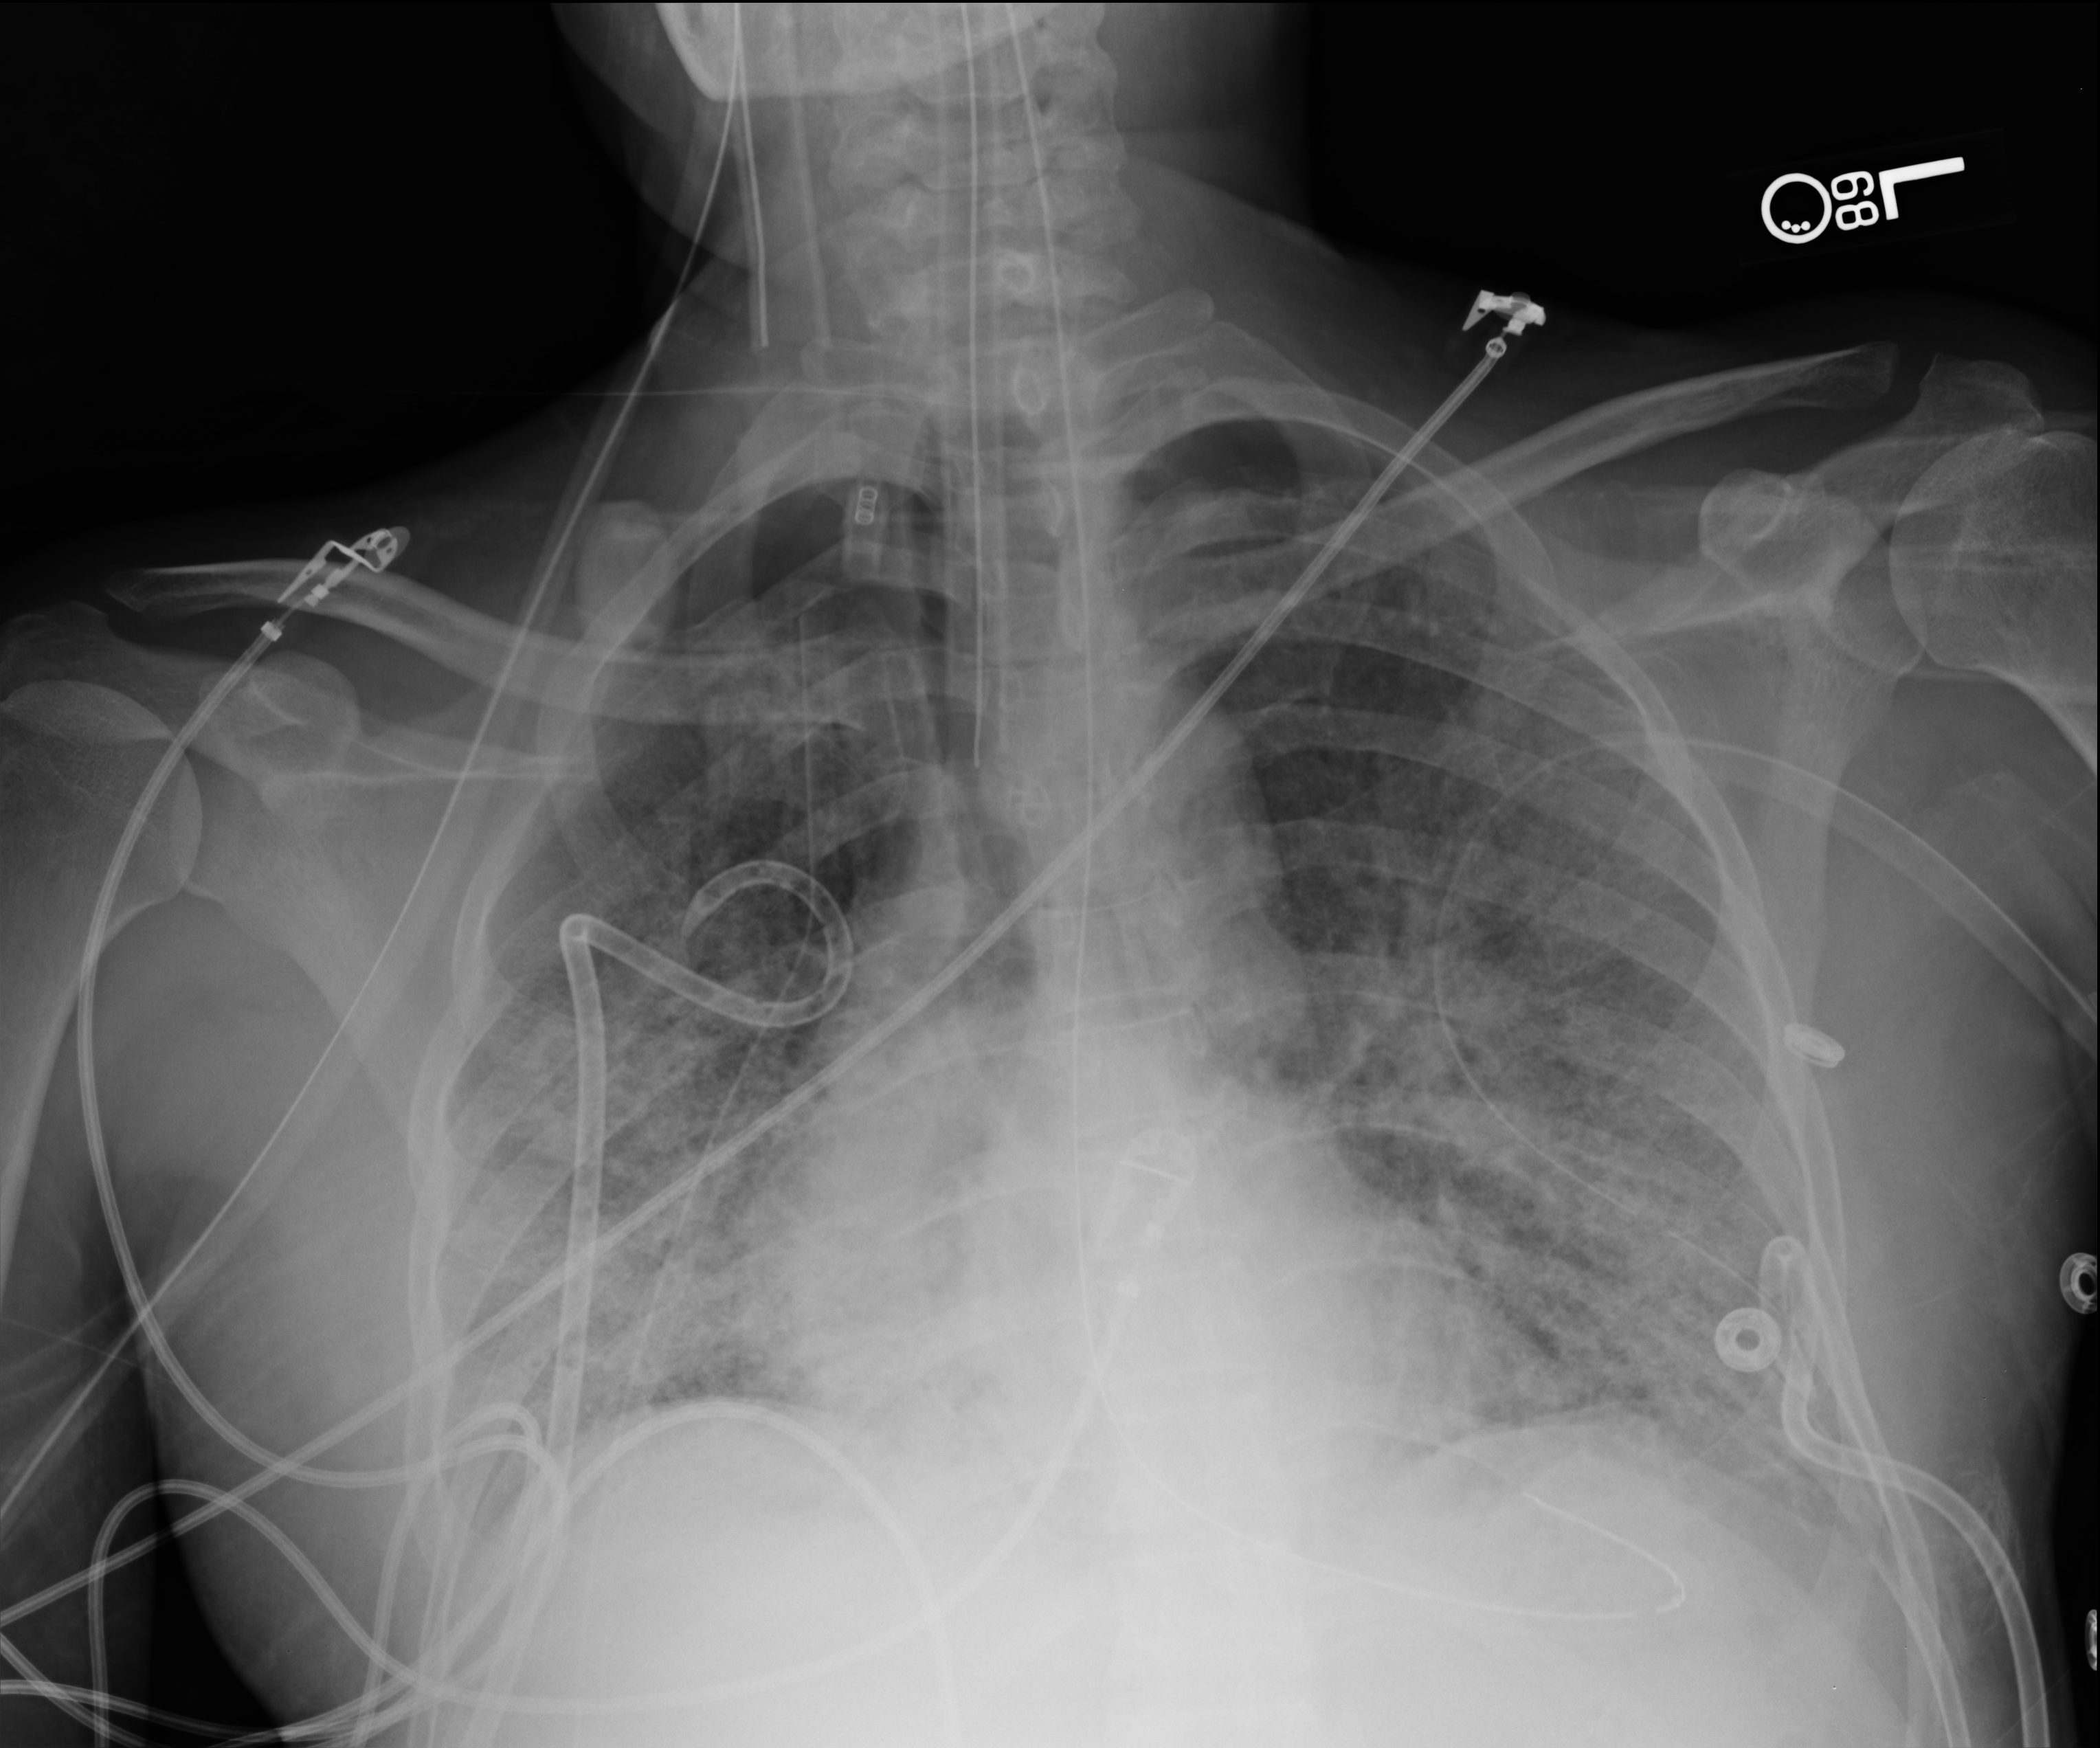
Chest X-ray (portable), anteroposterior (AP) projection. Adult patient hospitalised with COVID-19, age 18–59 years.
Admission-level facts for this patient (not findings on this image; timing relative to this image not recorded): mechanically ventilated during this hospital stay: yes; admitted to intensive care during this hospital stay: yes.